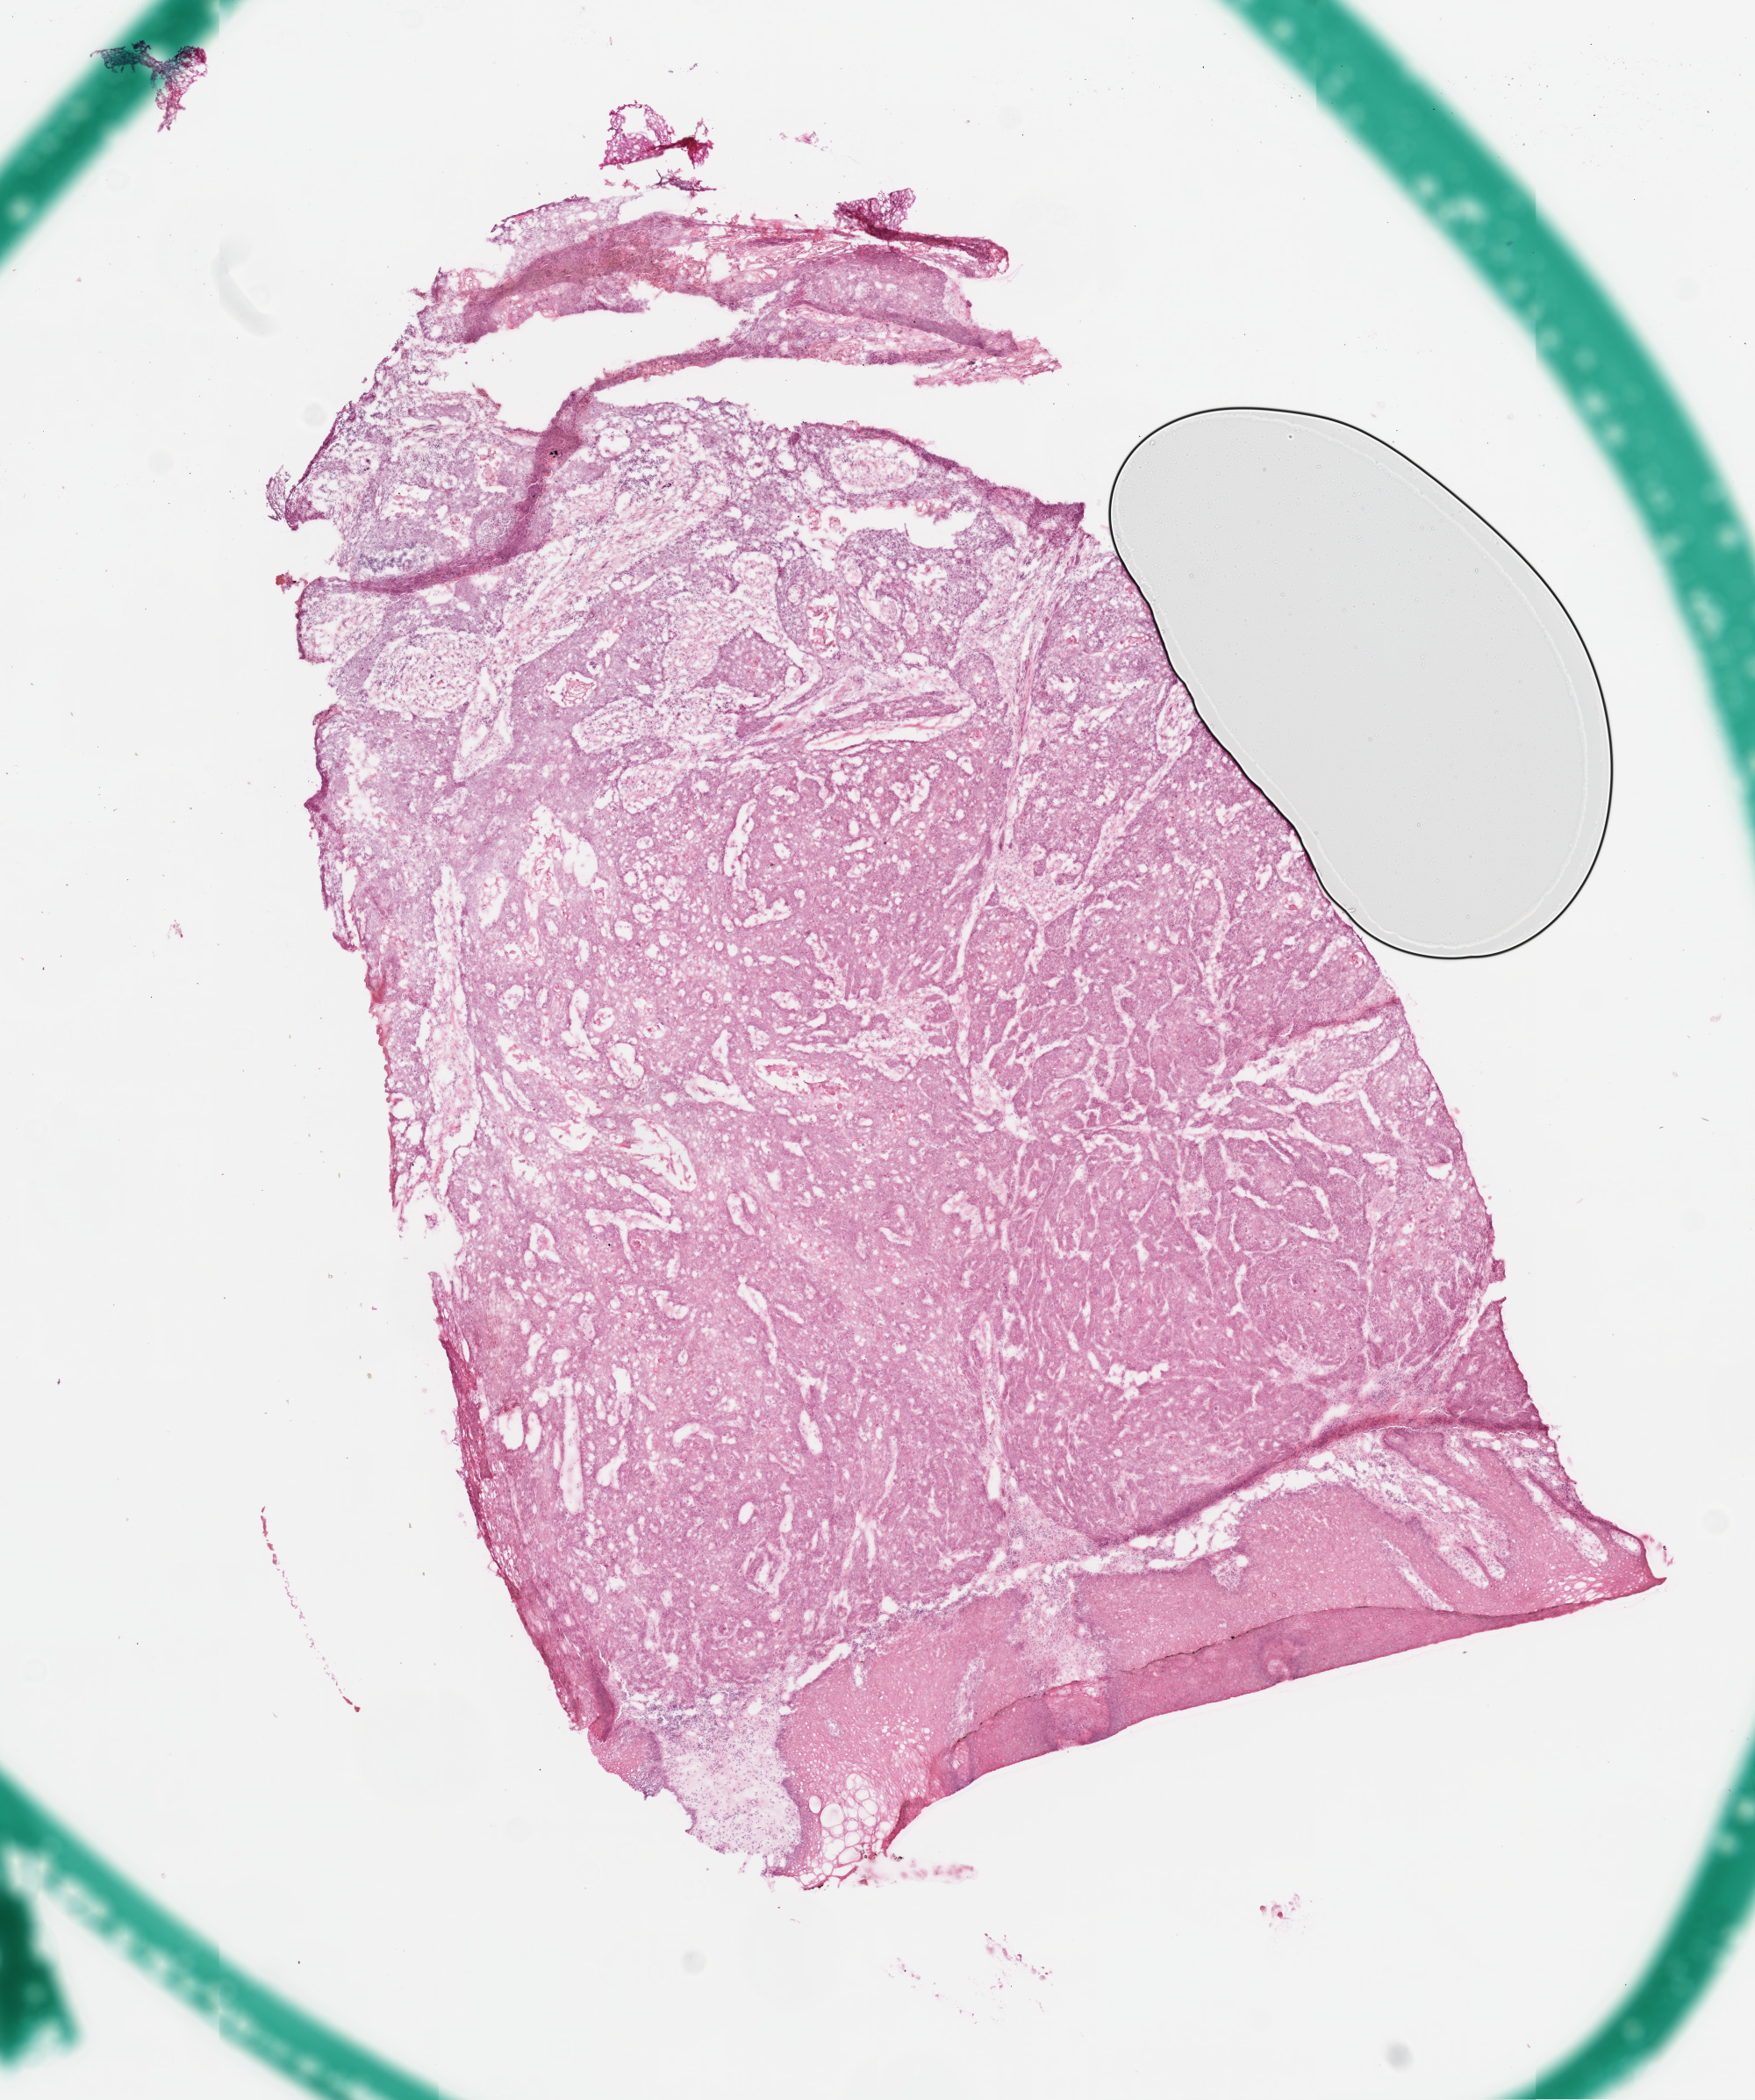
Hematoxylin and eosin (H&E) stained whole-slide image — a low-resolution overview of the entire scanned area, about 8.0 x 9.6 mm (slide scanned at 20x). Frozen section from the top of the tissue portion. Primary tumour sample from the head and neck. Patient: male, age at initial diagnosis 52 years. Histologic grade: G2 (moderately differentiated). Pathologist review of this section (percent, as recorded): tumour cells 90%, tumour nuclei 90%, normal cells 0%, stromal cells 5%, necrosis 5%. Inflammatory infiltration, as recorded: lymphocyte infiltration 1%.
• AJCC pathologic stage: IVA
• histologic diagnosis: Squamous cell carcinoma, NOS (tongue, NOS)